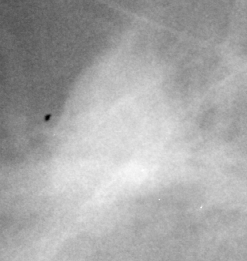
Cropped region of a digitized screen-film mammogram centred on a radiologist-marked abnormality; right breast; MLO view.
- Finding: mass, shape irregular, margins spiculated; BI-RADS assessment category 4; pathology result (as recorded, not read from the image): malignant.